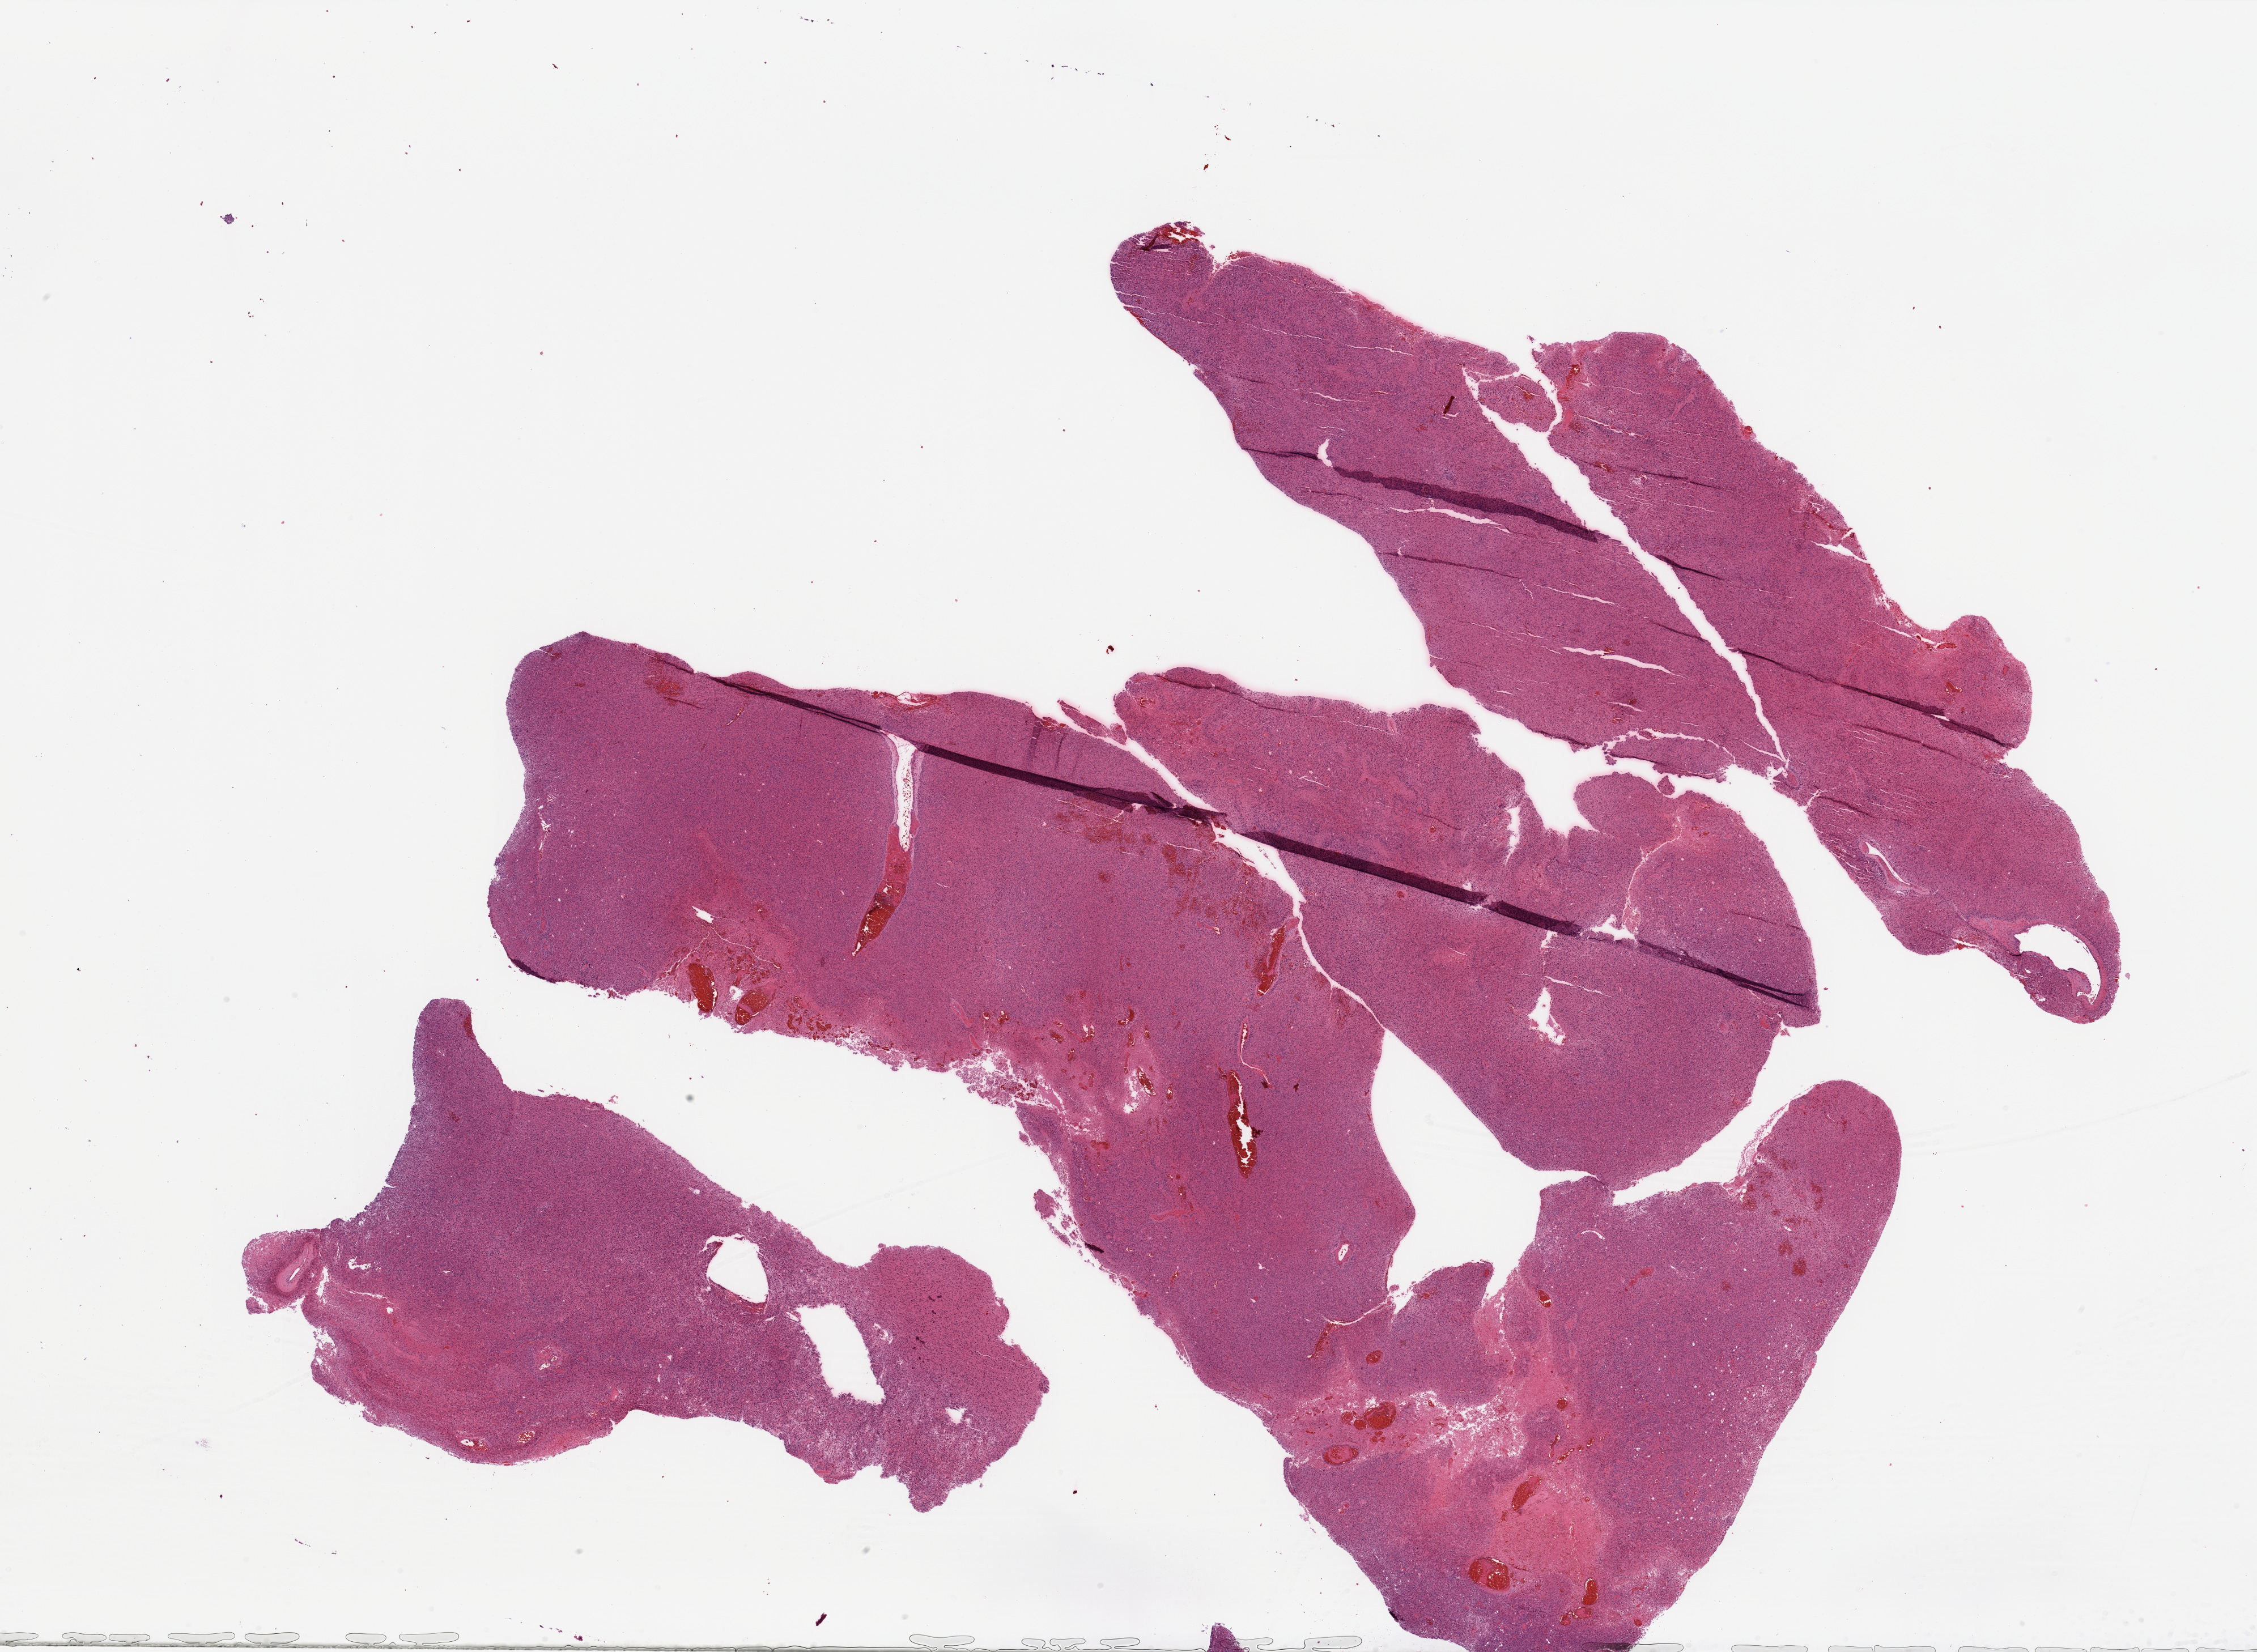
Whole-slide histology image, H&E-stained — shown as a low-resolution overview of the whole scanned area (about 31.5 x 23.1 mm, slide scanned at 20x); brain, tumour tissue. Patient: female, age 63 years.
* histologic diagnosis: Glioblastoma
* primary tumour site (as recorded): parietal lobe